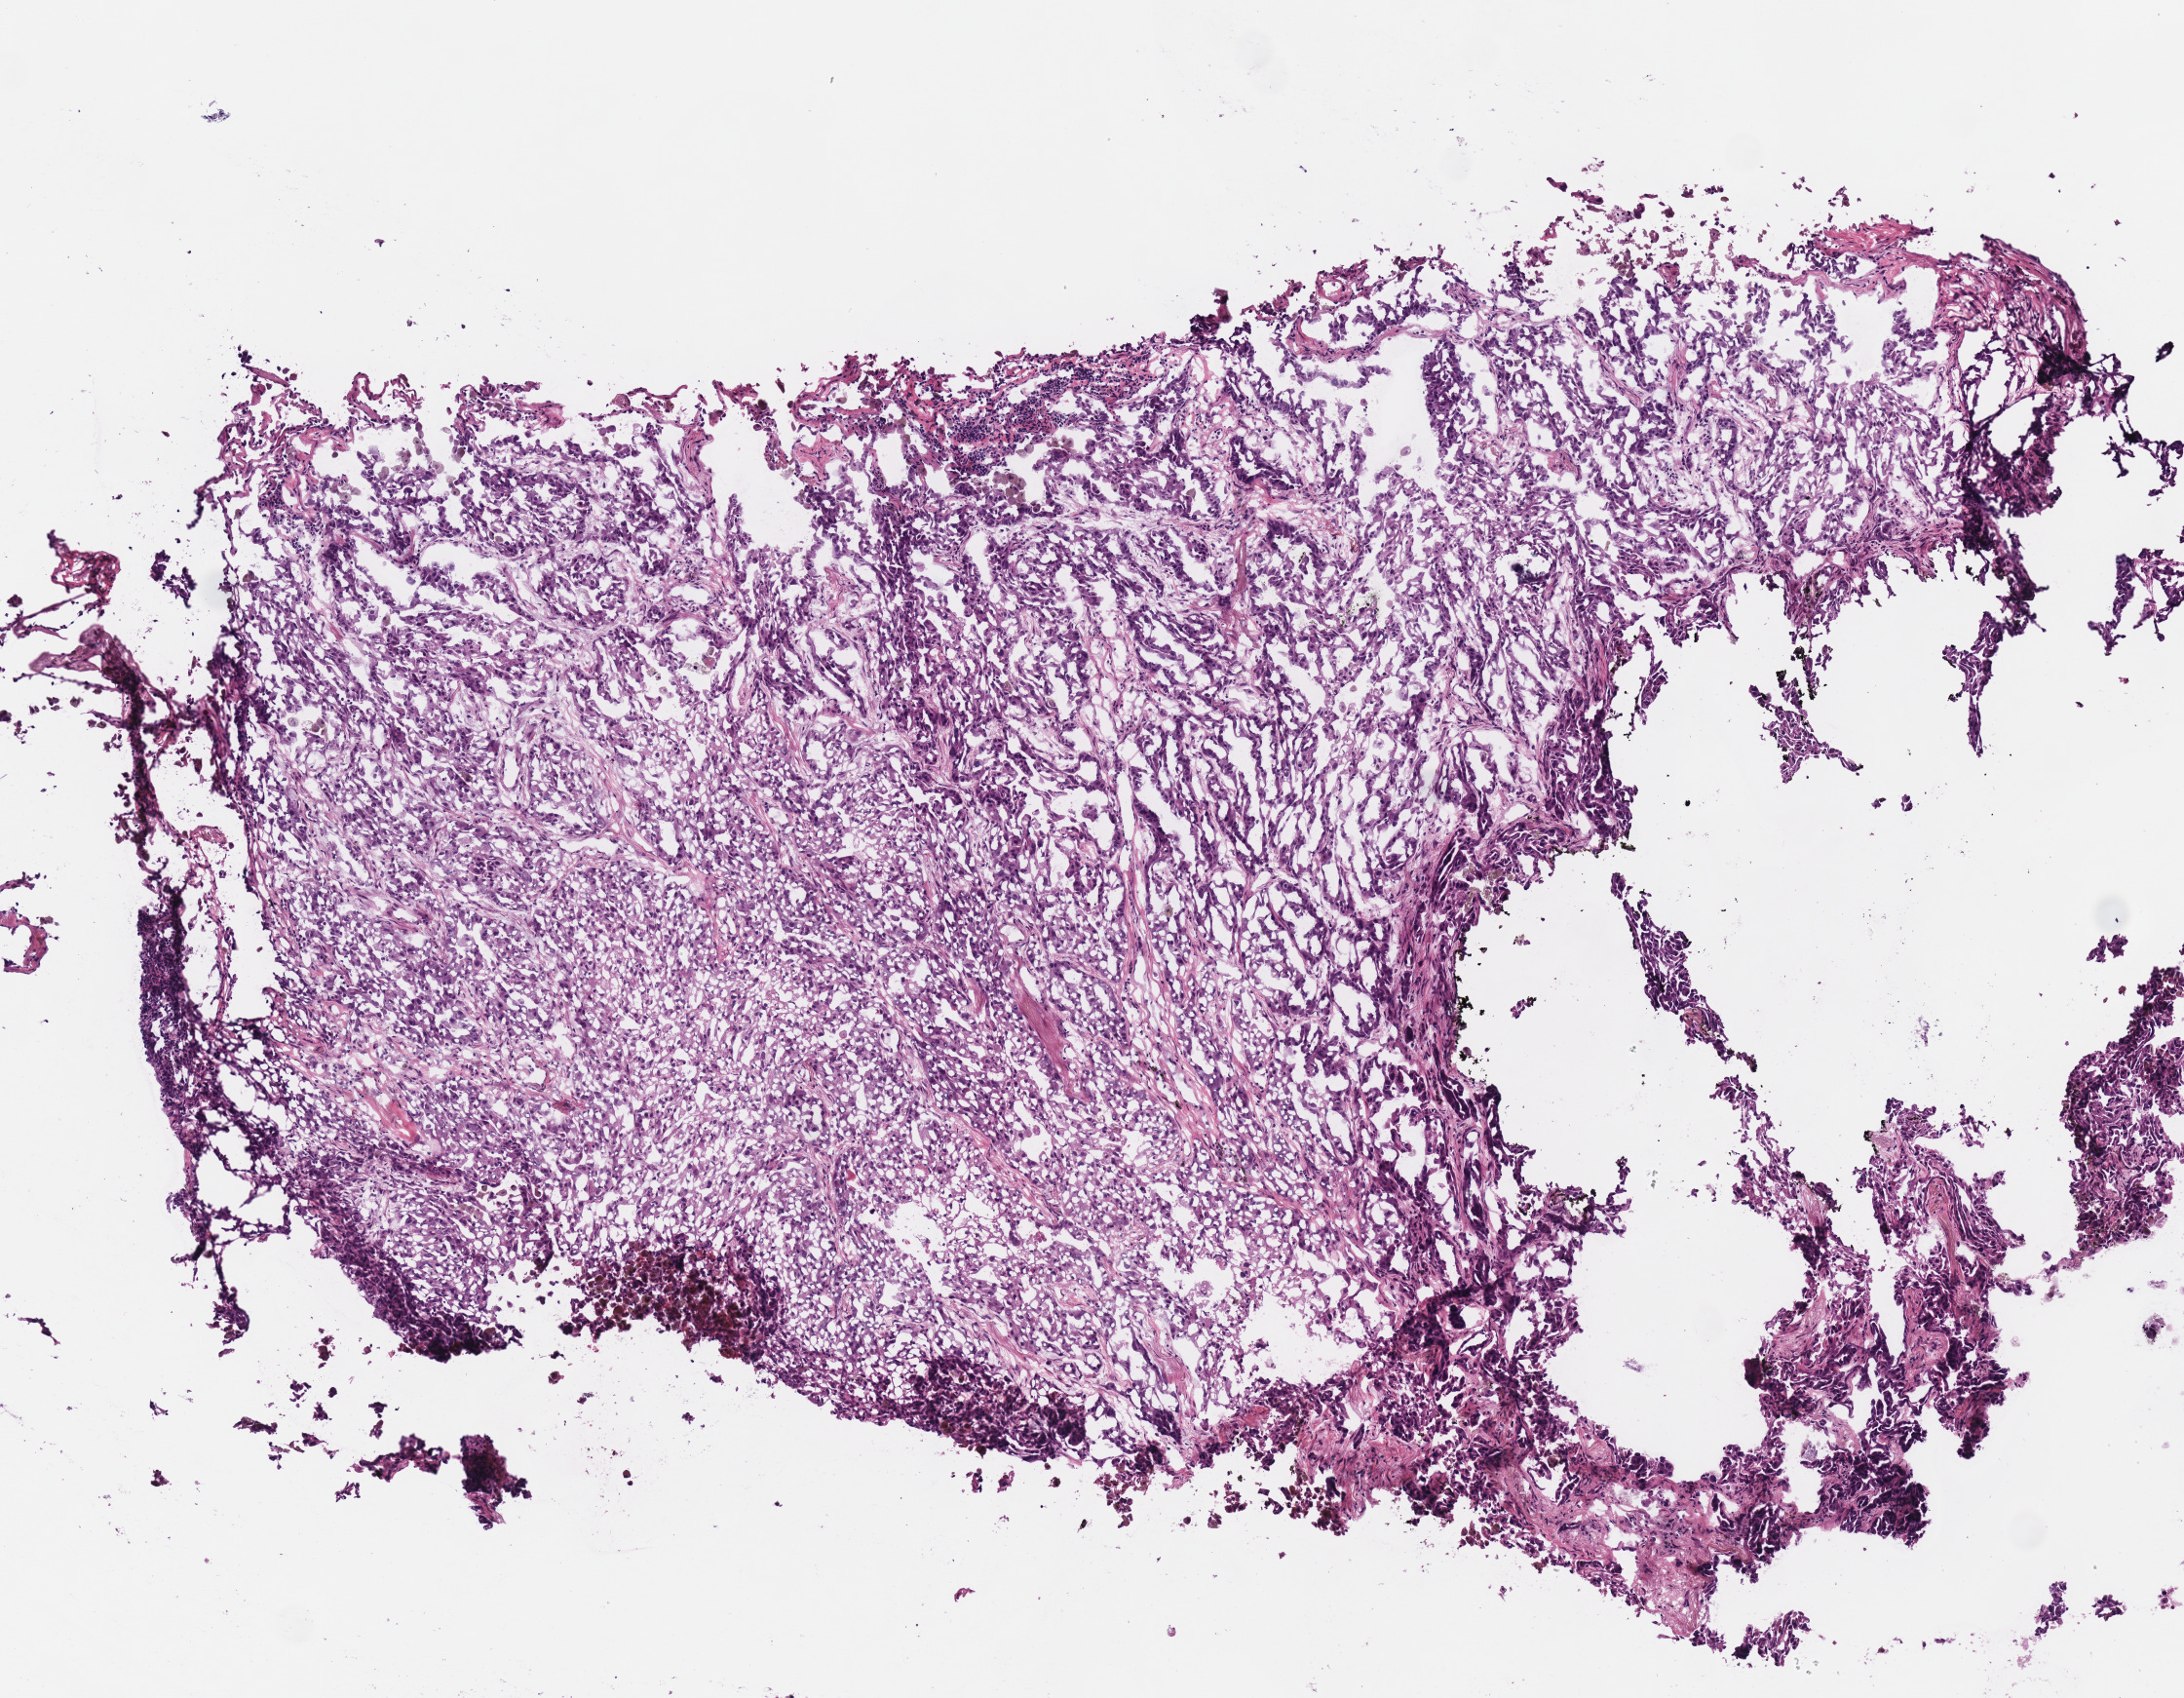
H&E whole-slide image, shown as a low-resolution overview of the whole scanned area (about 4.4 x 3.4 mm, slide scanned at 40x), frozen section from the top of the tissue portion, primary tumour sample from the lung. Patient: female, age at initial diagnosis 53 years. Slide review estimates, as recorded: tumour cells 90%, tumour nuclei 80%, normal cells 0%, stromal cells 10%, necrosis 0%.
- pathologic diagnosis: Adenocarcinoma, NOS (upper lobe, lung)
- TNM: T2 N0 M0
- AJCC pathologic stage: IB